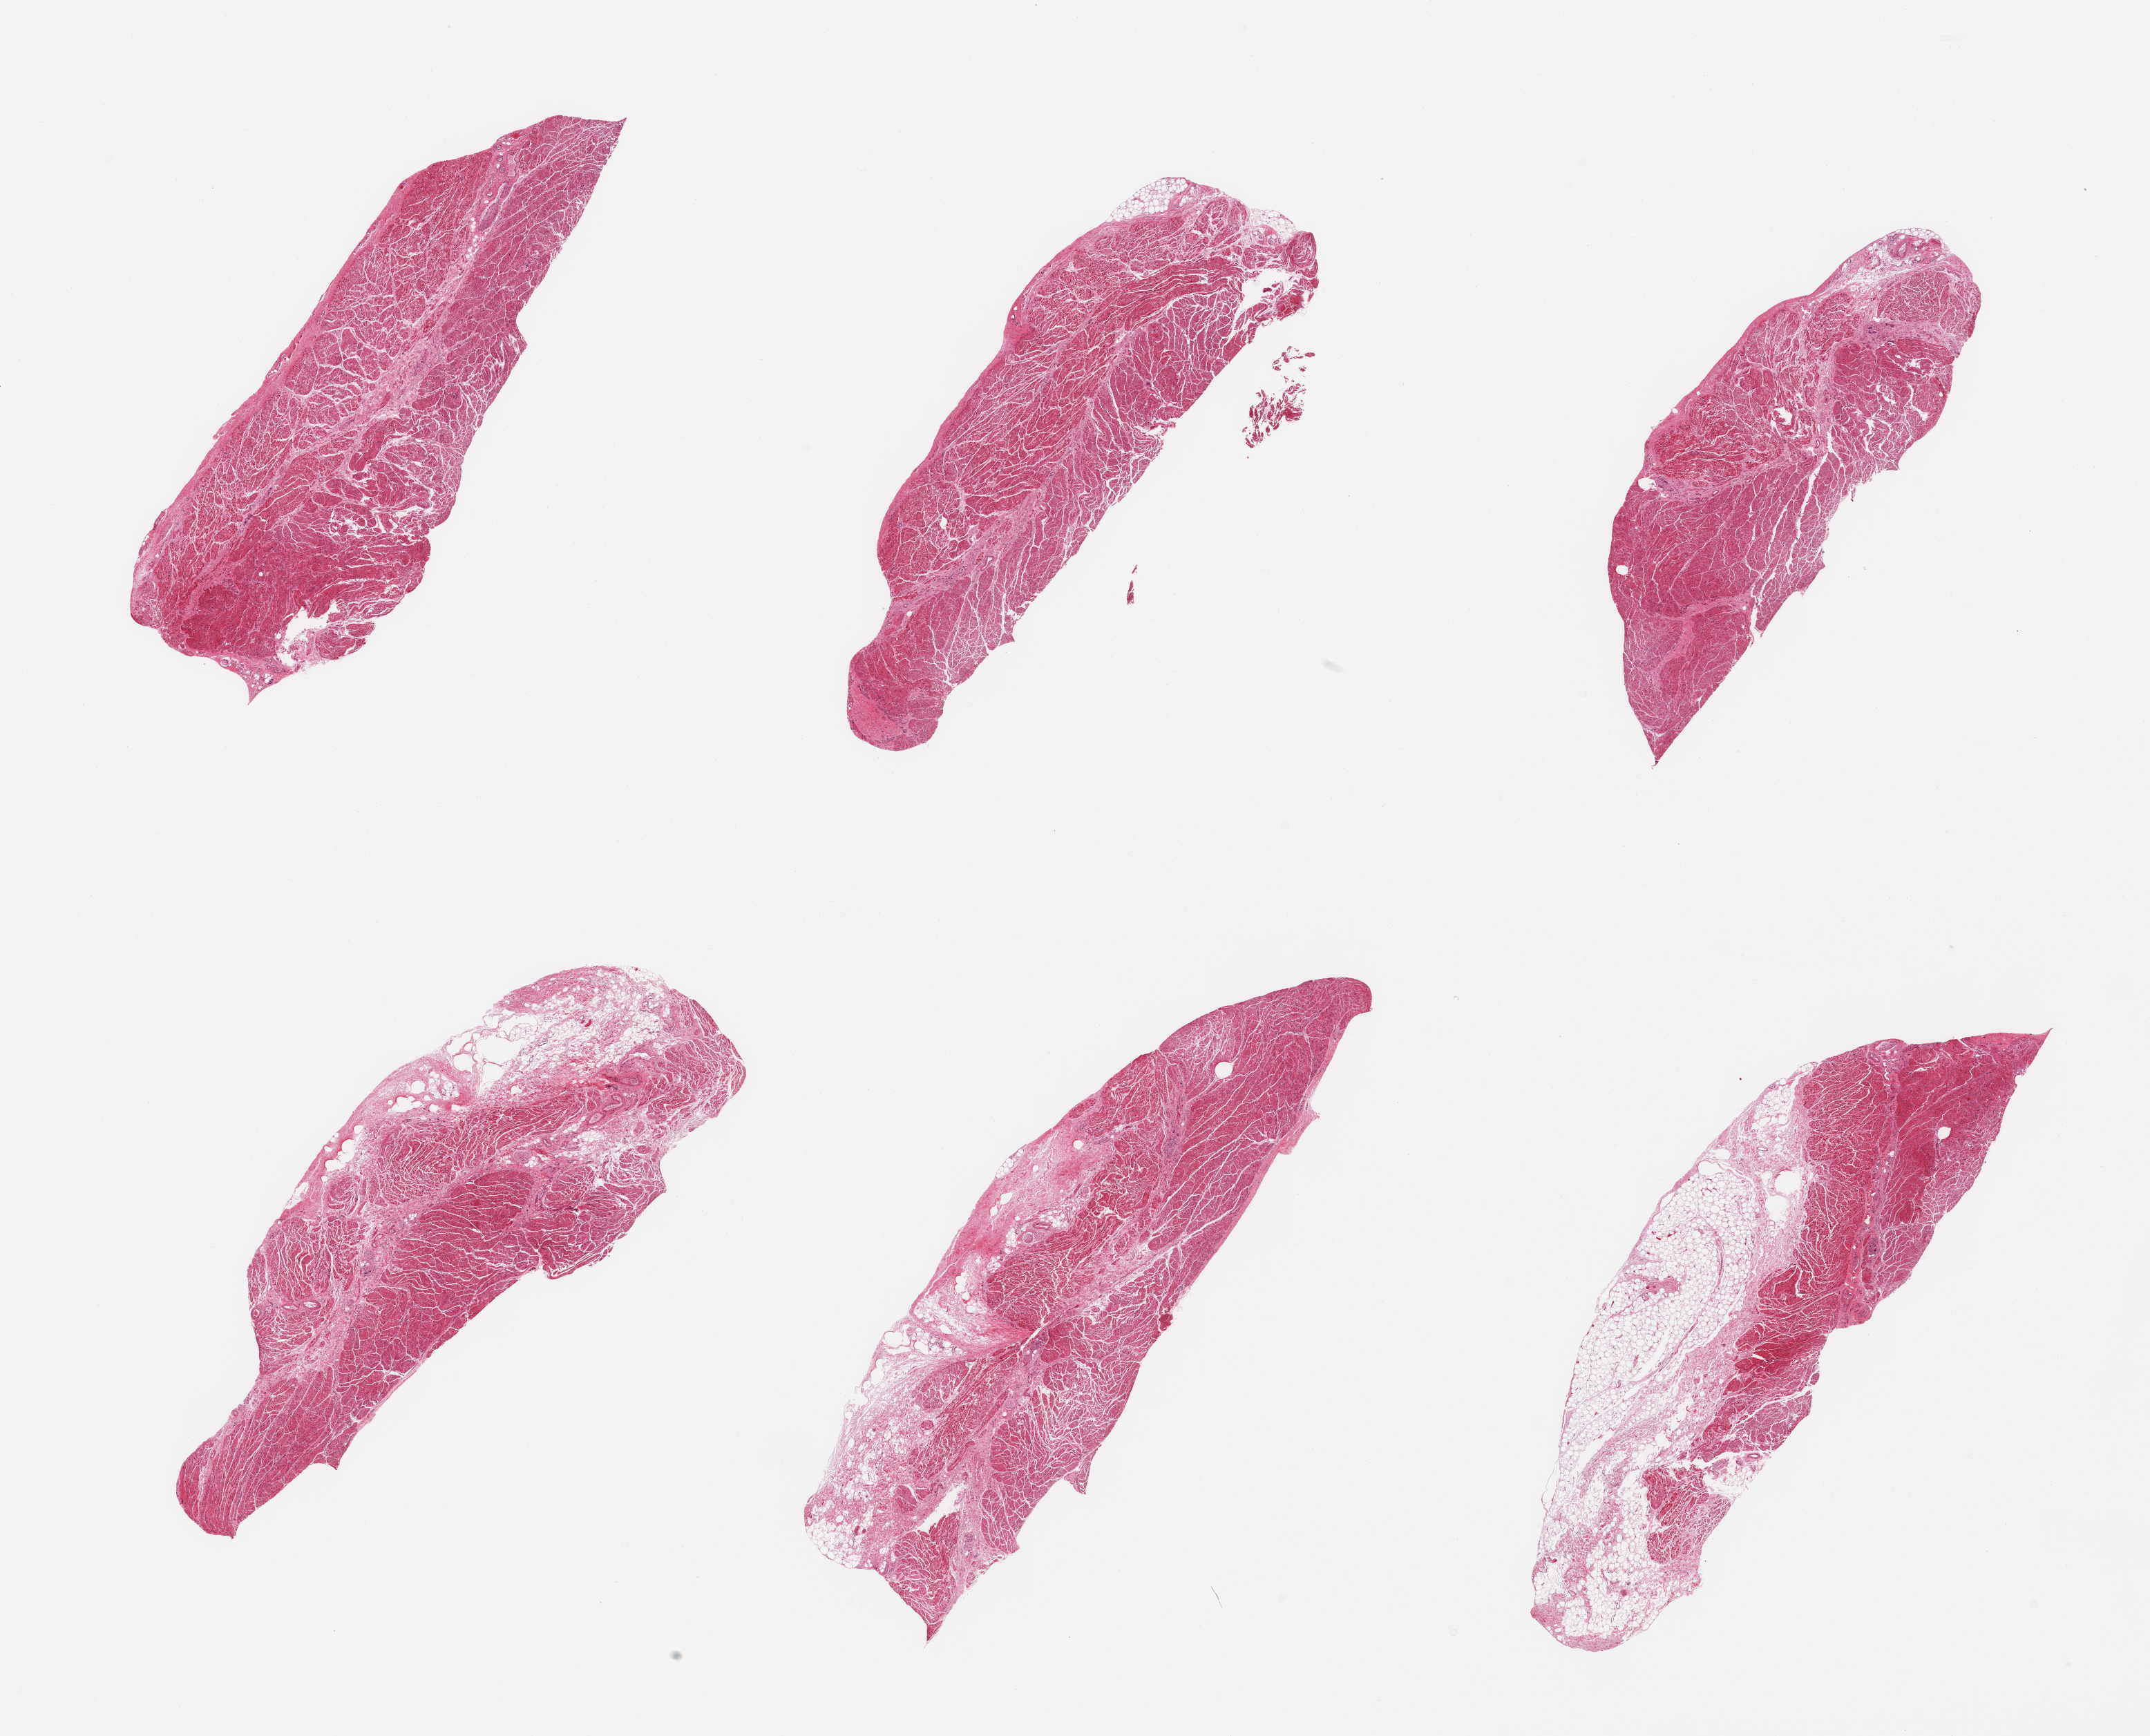
Digitized H&E-stained section — shown as a low-resolution overview of the whole scanned area (about 24.6 x 19.9 mm, from a 20x scan); PAXgene-fixed paraffin-embedded (PFPE) section; target tissue: gastroesophageal junction; tissue donor sample. Male donor.
Review note (as recorded): 6 pieces, confirmed target muscularis, adherent nubbins of fat up to ~1.5mm.